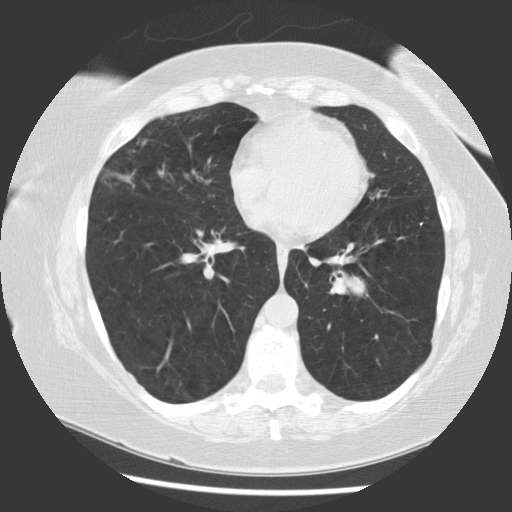
Axial slice from a low-dose chest CT screening exam; baseline annual screen; lung window (W 1500 / L -600 HU); 2.5 mm slice thickness. Female, age 58 years at enrolment. Former smoker at enrolment.
Expert-annotated lung lesion, bounding box <325,257,396,321> (left, top, right, bottom; pixels). Reader record for this screening exam (exam-level; its link to the box is not recorded): non-calcified nodule or mass ≥4 mm, left lower lobe, 22 × 15 mm, smooth margins, soft tissue attenuation.